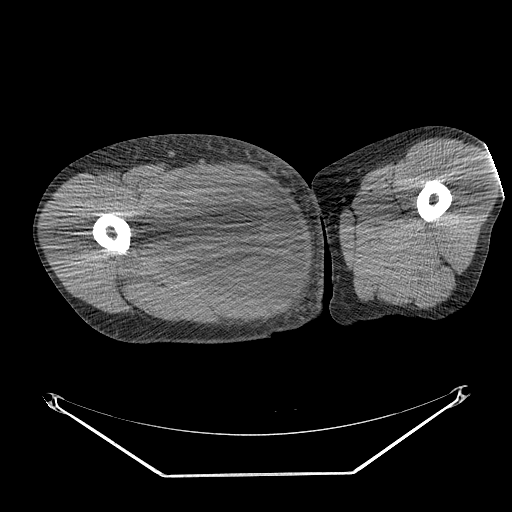
CT of an extremity soft-tissue mass (from a PET/CT study), one axial slice. Position 256 of 311 along the scan axis. Reconstruction kernel STANDARD. 140 kVp. Soft-tissue window (W 400 / L 40 HU). 512 × 512 image matrix, field of view 500 × 500 mm. Male patient. From the clinical record (not read from this slice): histological type: undifferentiated - pleiomorphic; grade: high; site of the primary tumour: right thigh.
Annotated regions visible in this slice (expert contour drawn on MRI and transferred to this co-registered scan by the dataset authors):
- gross tumour volume including surrounding oedema: bounding box (x1, y1, x2, y2) in pixels: (139, 169, 264, 275)
- gross tumour volume (mass): (153, 169, 264, 270)